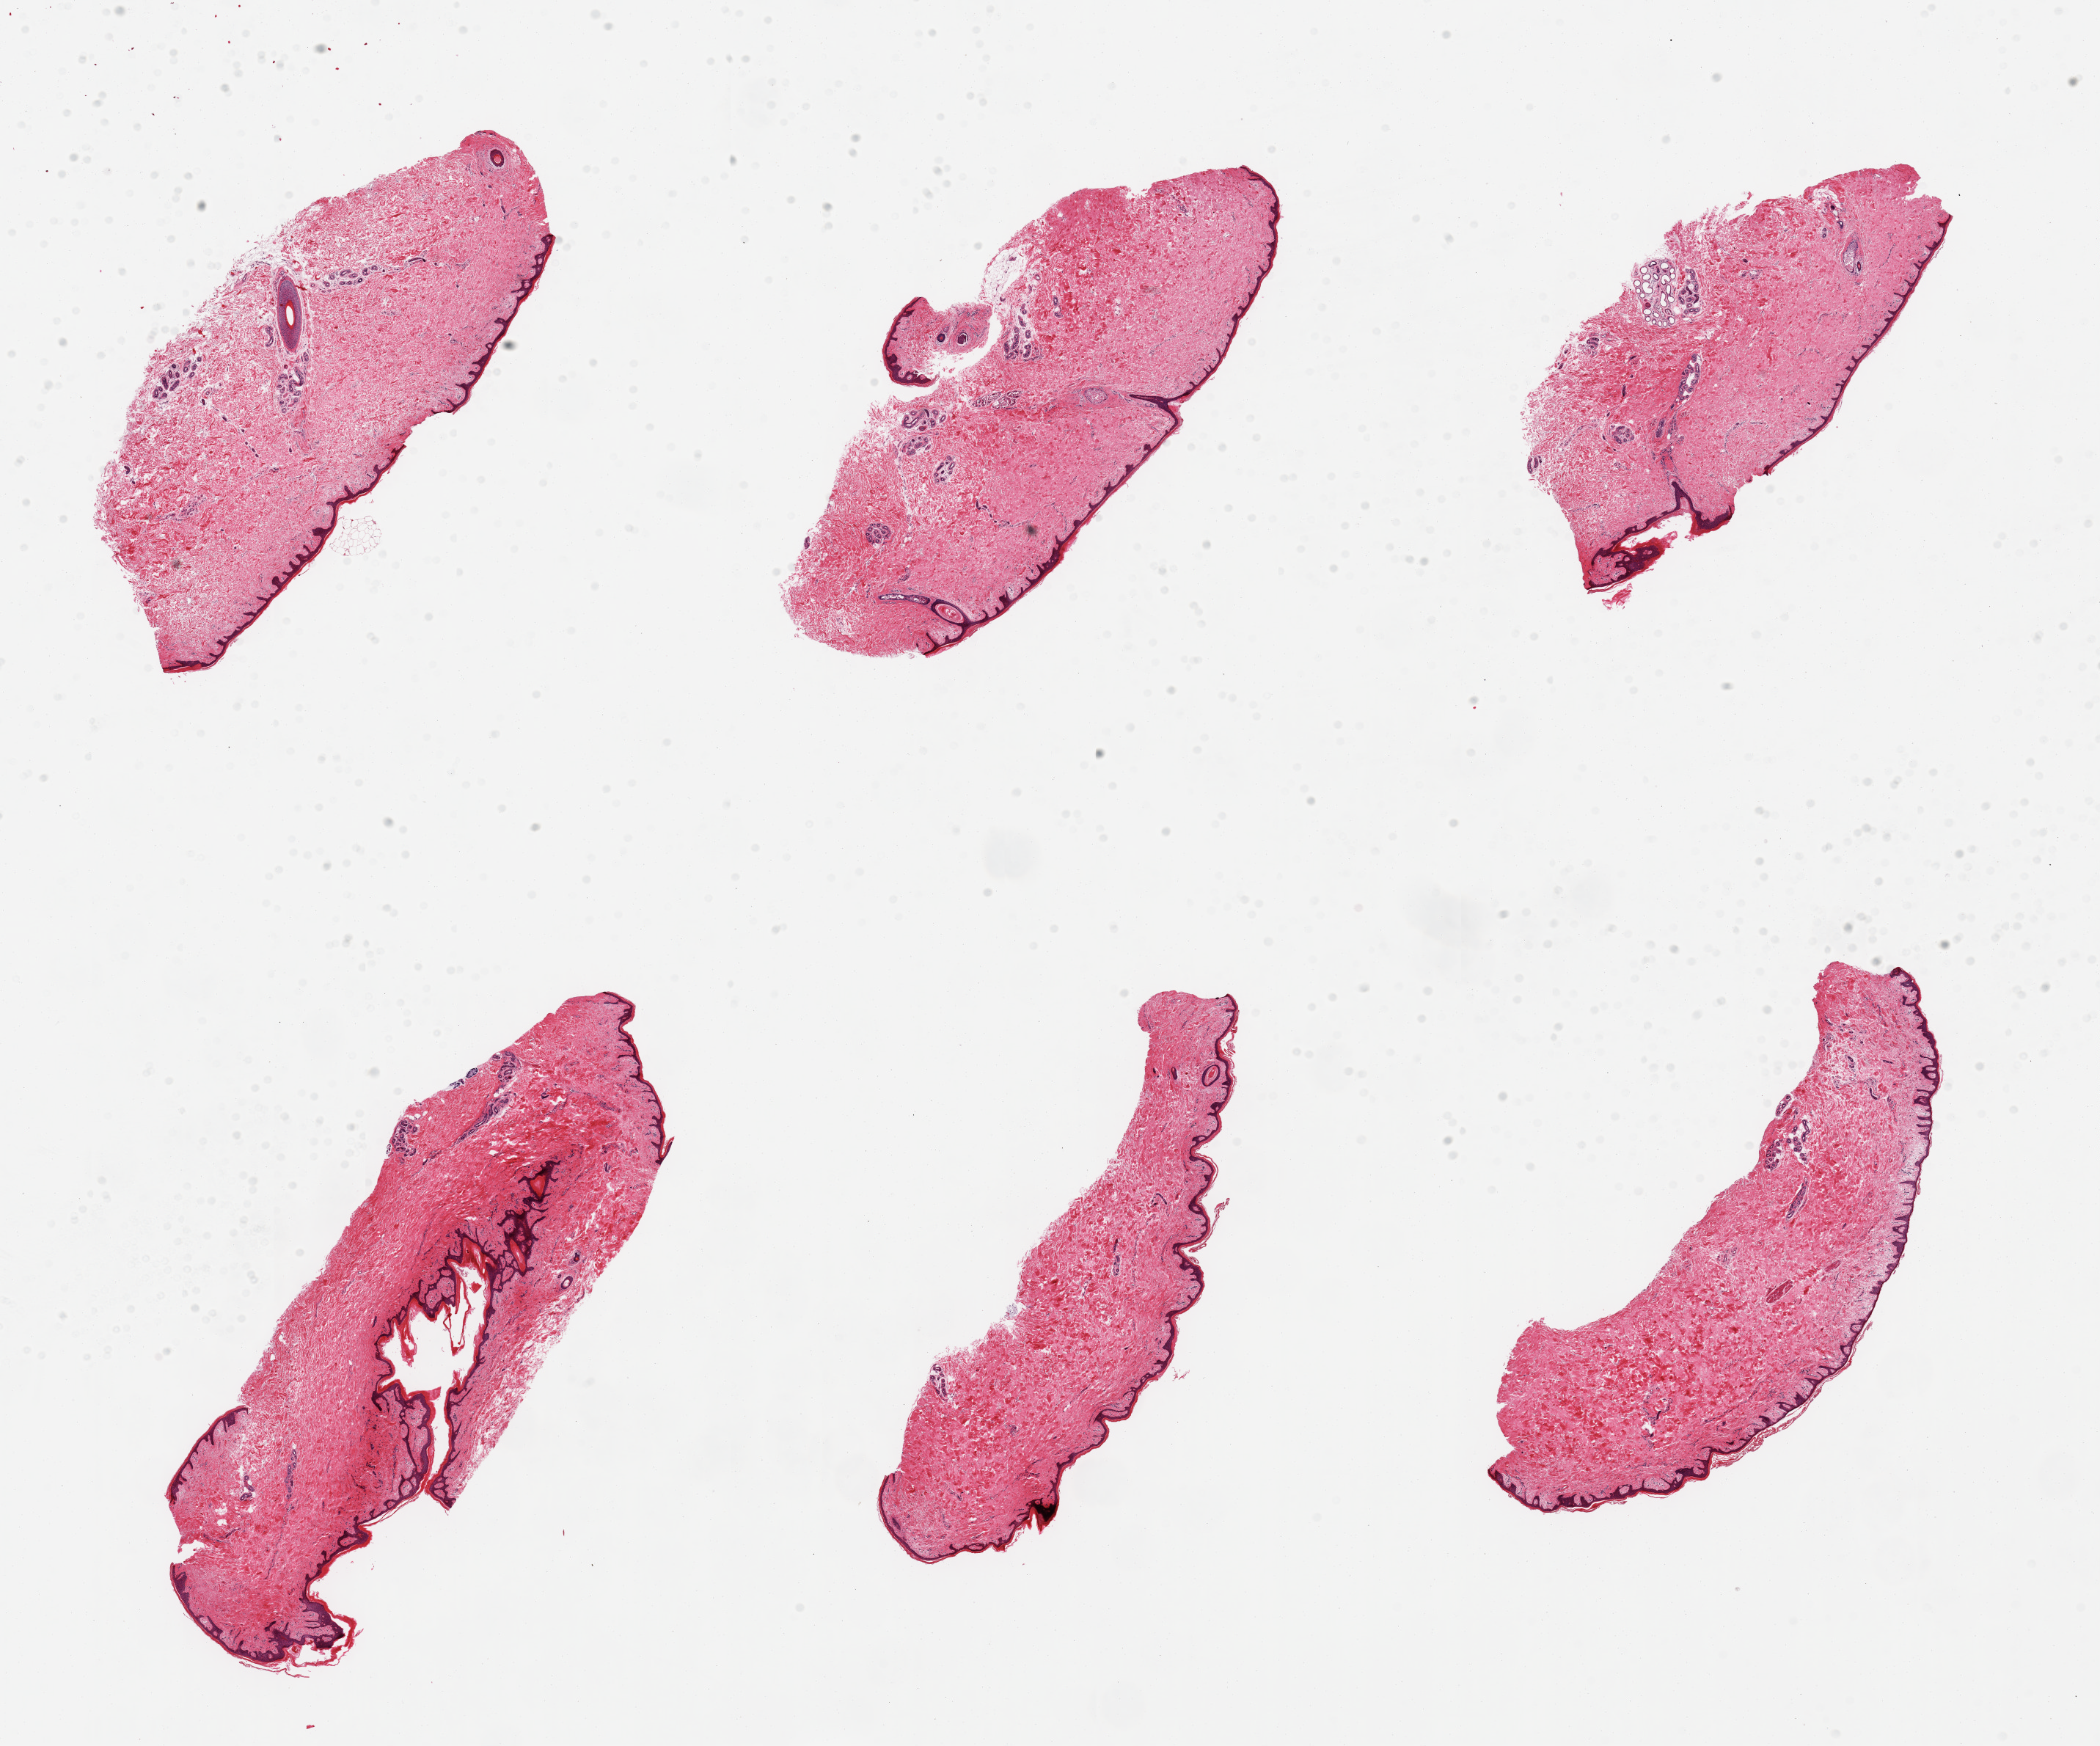
Digitized hematoxylin and eosin (H&E)-stained section — a low-resolution overview of the entire scanned area, about 22.6 x 18.8 mm, PAXgene-fixed, paraffin-embedded tissue, target tissue: skin of suprapubic region, tissue donor sample.
Pathologist's review note for this sample: 6 pieces; well trimmed; no dermall fat.